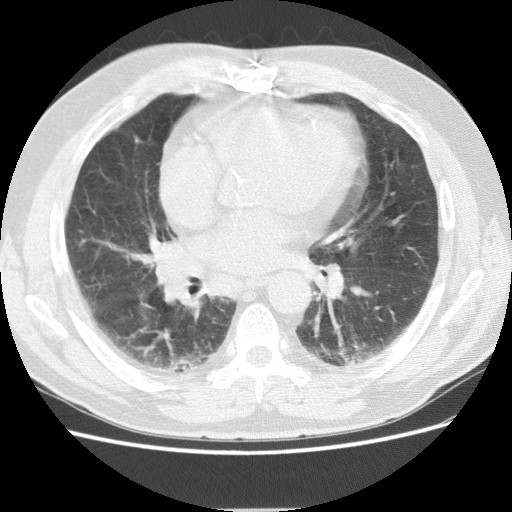
Low-dose screening chest CT, axial slice, baseline annual screen, lung window (W 1500 / L -600 HU), 2.5 mm slice thickness, standard (soft-tissue) reconstruction kernel (STANDARD), slice 71 of 155 in the series. Male, age 72 years at enrolment. Former smoker at enrolment.
Expert-annotated lung lesion, bounding box <145,233,195,271> (left, top, right, bottom; pixels). Screening reader's record for this exam: no non-calcified nodule ≥4 mm recorded. Official screen result: negative screen, minor abnormalities not suspicious for lung cancer.